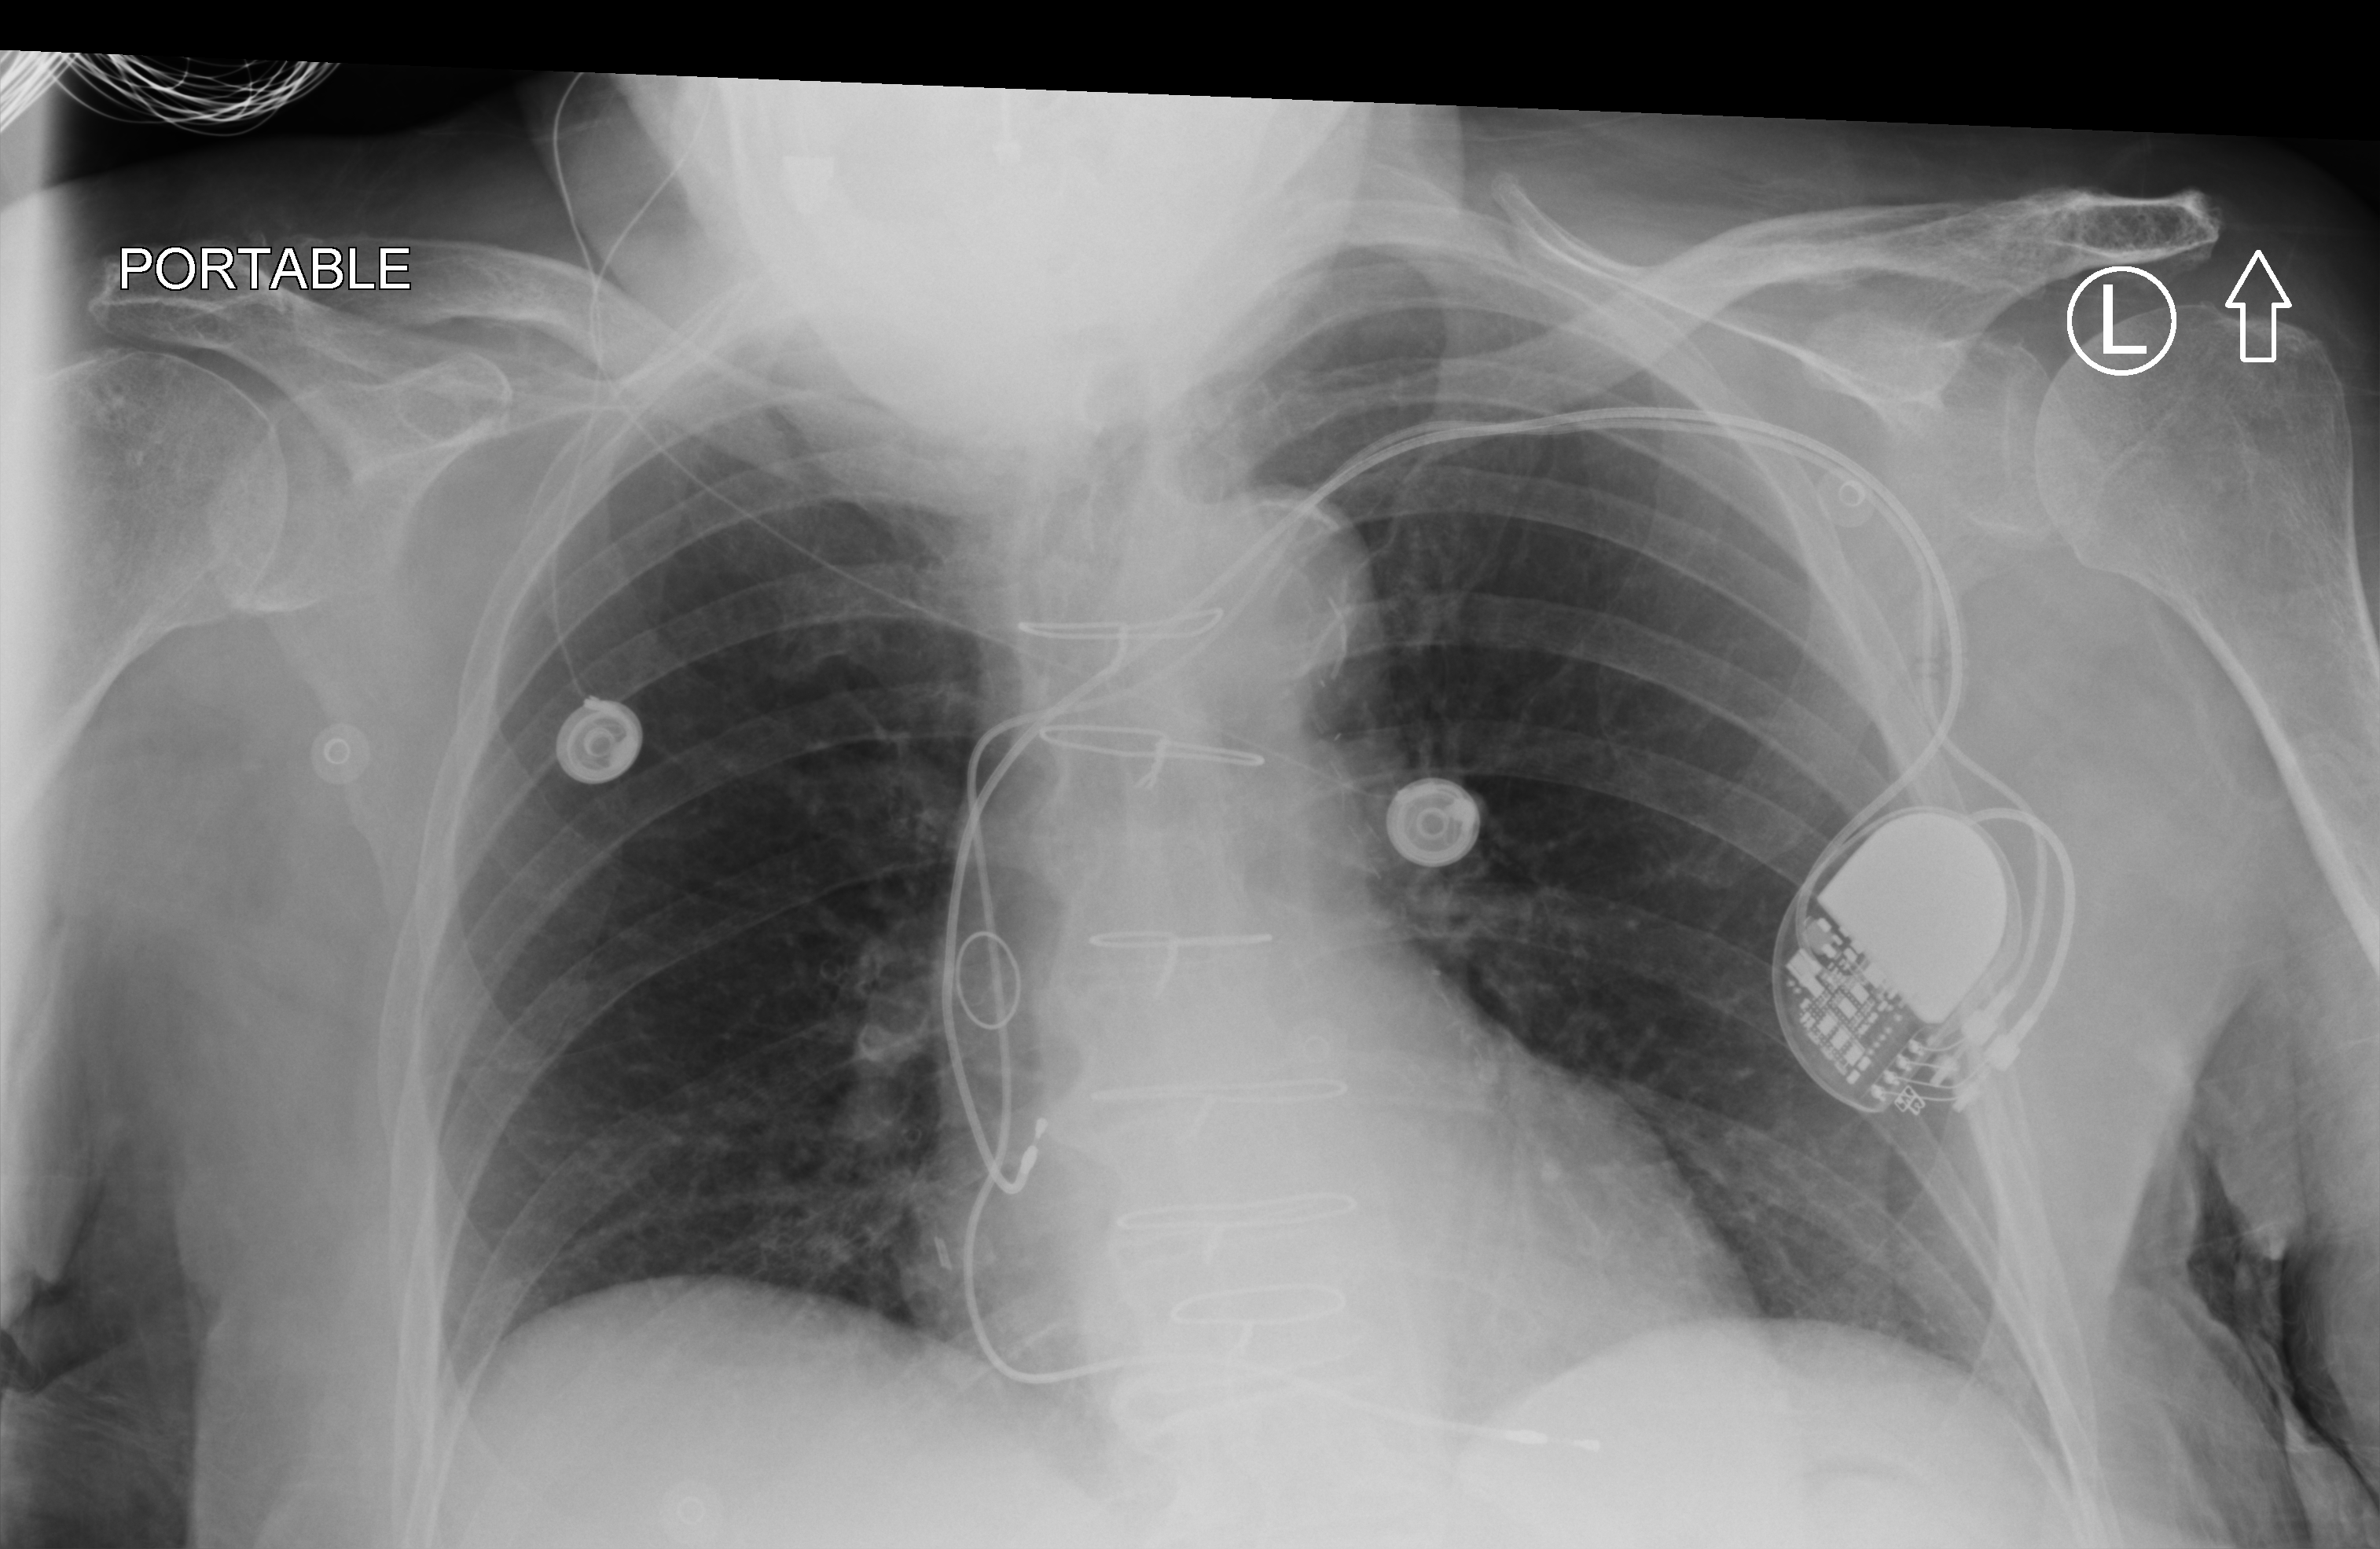
Portable chest radiograph, anteroposterior (AP) projection. Female patient hospitalised with COVID-19, age 75–90 years.
From the hospital-stay record, not from the radiograph (when in the stay this image was taken is not recorded): admitted to intensive care during this hospital stay: no.